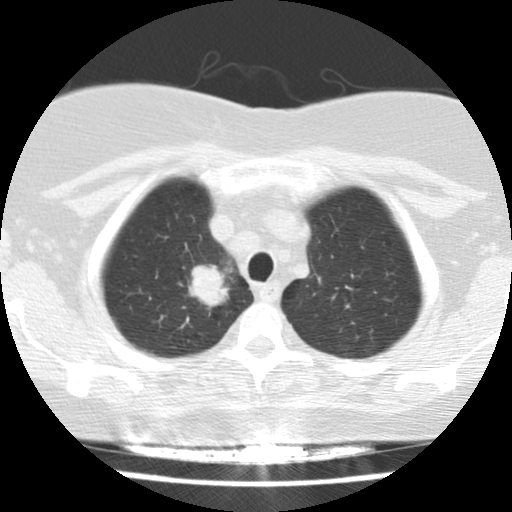
Low-dose screening chest CT, one axial slice. Slice 127 of 148 in the series (ordered by position). 120 kVp. Lung window (W 1500 / L -600 HU). 512 × 512 image matrix.
Annotated regions visible in this slice (outlined manually by an expert reader):
- lesion 1 (tumor, upper lobe of right lung): bounding box <189,264,229,308> (left, top, right, bottom; pixels)